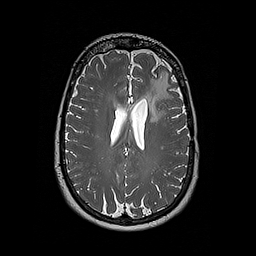
Brain MRI from a brain-tumour surgery series, one axial slice. Slice 117 of 192 in the series (ordered by position). 1 mm slice thickness. 256 × 256 image matrix, field of view 250 × 250 mm. Case-level facts recorded for this patient, not image findings: histopathology: Oligodendroglioma; WHO grade: 2; IDH mutation: yes; tumour location: Left Frontal.
Annotated regions visible in this slice (outlined manually by an expert reader):
- tumour: bounding box <145,77,162,122> (left, top, right, bottom; pixels)